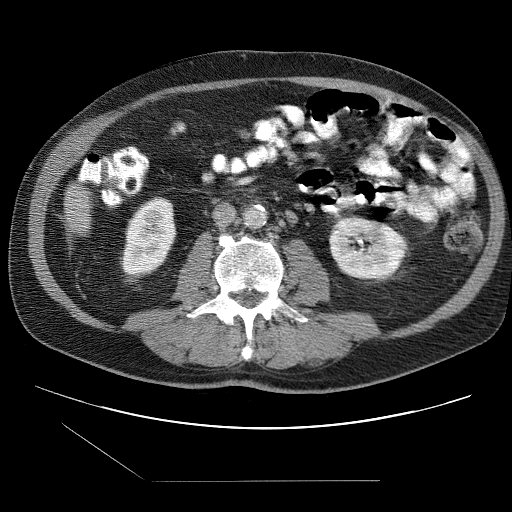
Contrast-enhanced abdominal CT (liver protocol), one axial slice; slice 9 of 109 in the series (ordered by position); one of 2 acquisitions stored at this slice position; soft-tissue window (W 400 / L 40 HU); 512 × 512 image matrix, field of view 400 × 400 mm. Case-level facts recorded for this patient, not image findings: diagnosis: hepatocellular carcinoma (patient treated with transarterial chemoembolisation; whether this scan precedes or follows treatment is not stated here); TNM stage (as recorded): Stage-IIIB; Child-Pugh class: A; tumour differentiation: well differentiated; tumour nodularity: multinodular.
Outlined on this slice (semi-automatic segmentation, software-assisted and operator-edited):
- liver parenchyma outside the tumour (the mass and vessels are separate outlines, so this box may not span the whole liver): box from (x=66, y=186) to (x=90, y=231) px